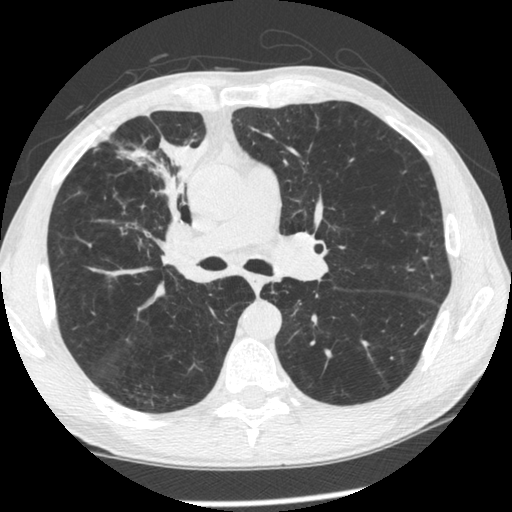
Low-dose screening chest CT, one axial slice. Position 140 of 261 along the scan axis. Lung window (W 1500 / L -600 HU). 1.25 mm slice thickness. 512 × 512 image matrix.
Structures marked on this image (expert manual segmentation):
- lesion 1 (tumor, upper lobe of right lung): bounding box [x1, y1, x2, y2] px = [119, 138, 208, 236]